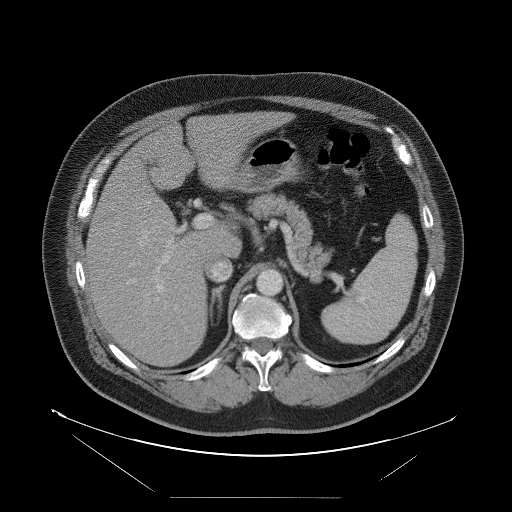
Contrast-enhanced abdominal CT, one axial slice; position 59 of 114 along the scan axis; 120 kVp; intravenous contrast given; soft-tissue window (W 400 / L 40 HU); 5 mm slice thickness; 512 × 512 image matrix, field of view 500 × 500 mm. Male patient, age 61 years. From the clinical record (not read from this slice): diagnosis: colorectal cancer liver metastases, imaged before liver resection; multiple liver metastases: no; largest metastasis: 6.5 cm; disease in both lobes: yes.
Outlined on this slice (outlined manually by an expert reader):
- hepatic veins: bounding box (x1, y1, x2, y2) in pixels: (139, 231, 154, 246)
- liver: (87, 112, 281, 366)
- planned liver remnant (the part of the liver to remain after resection): (145, 112, 281, 244)
- portal vein (with intrahepatic branches): (153, 215, 211, 302)